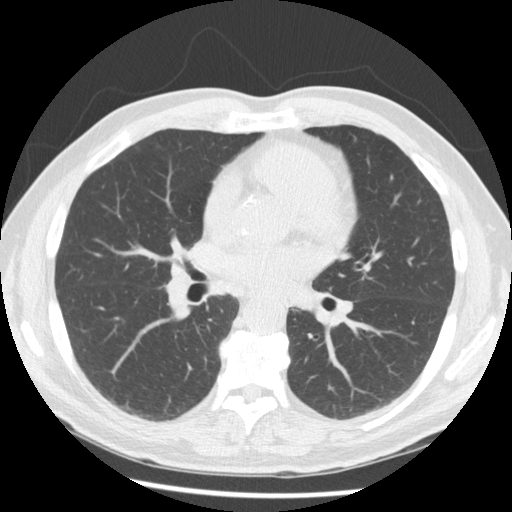
Chest CT (low-dose screening protocol), one axial image, baseline screening round, lung window (W 1500 / L -600 HU), 2.5 mm slice thickness, standard (soft-tissue) reconstruction kernel (STANDARD), 120 kVp, 512 × 512 image matrix. Male, age 62 years at enrolment.
Lesion marked by an expert reader, bounding box [x1, y1, x2, y2] px = [156, 247, 220, 308]. Screening reader's record for this exam: no non-calcified nodule ≥4 mm recorded. Later outcome: lung cancer diagnosed 146 days after this screen — small cell carcinoma, NOS, right hilum, mediastinum, poorly differentiated (G3), stage IV (AJCC 6th edition).